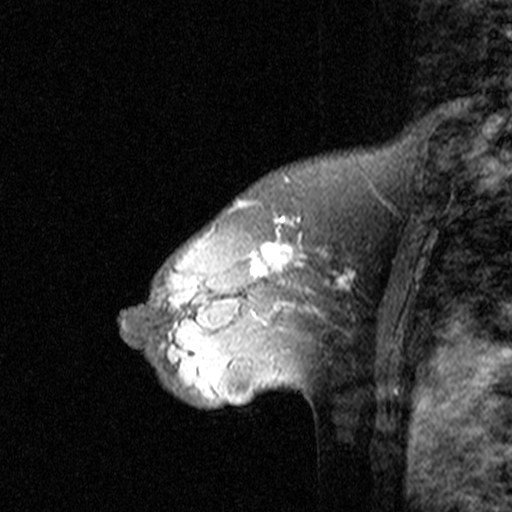
Breast MRI (dynamic contrast-enhanced), one sagittal slice. Position 30 of 44 along the scan axis. Dynamic contrast-enhanced study with each time point stored as its own series, time point 2 of 3 at this slice position (early post-contrast, ordered by acquisition time). 1.5 T. TE 4.5 ms, TR 11 ms. 3 mm slice thickness. 512 × 512 image matrix, field of view 200 × 200 mm. Patient: female, 46 years. Case-level facts recorded for this patient, not image findings: setting: breast cancer imaged before/during neoadjuvant chemotherapy; receptor status: HER2-positive.
Structures marked on this image (semi-automatically segmented with operator editing):
- analysis volume of interest (the breast-tissue region the enhancement analysis was run in; not a lesion): bounding box [x1, y1, x2, y2] px = [144, 172, 359, 393]
- tumour enhancement mask (voxels above the 90 % enhancement threshold inside the analysis volume of interest): [159, 212, 353, 356]